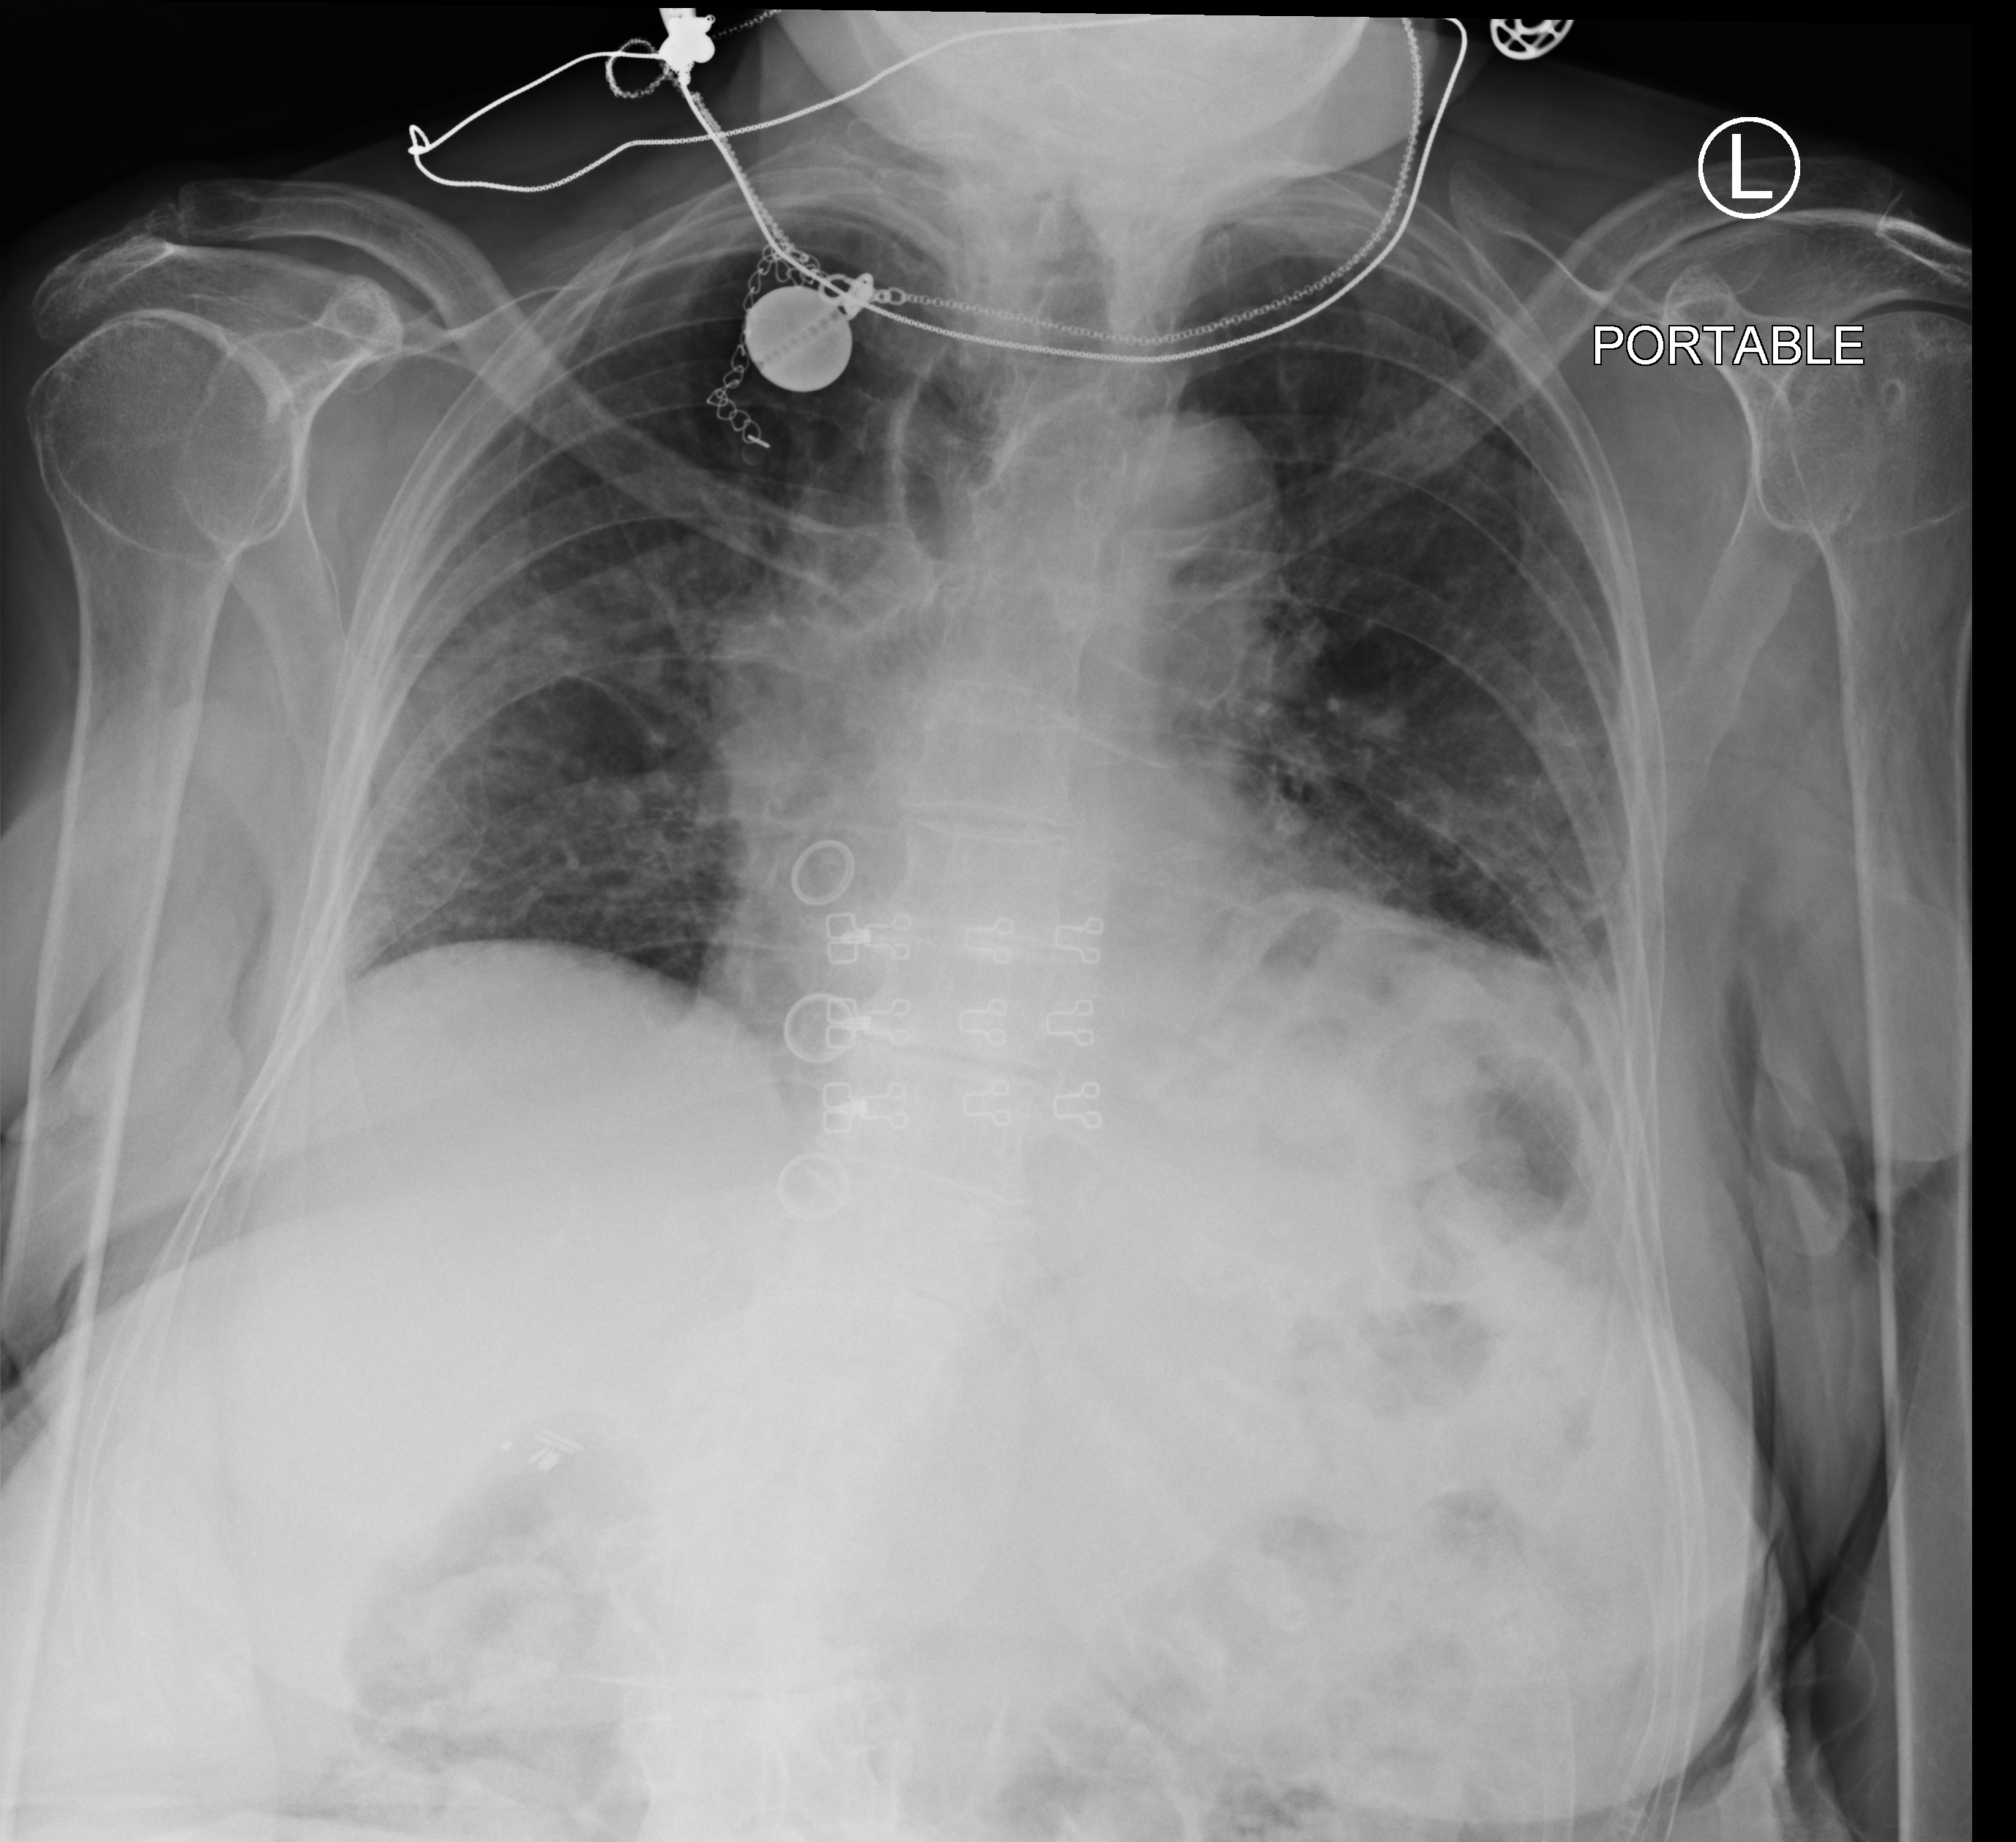
Bedside chest radiograph (computed radiography), anteroposterior (AP) projection. Patient hospitalised with COVID-19; female, aged 75–90 years.
From the hospital-stay record, not from the radiograph (when in the stay this image was taken is not recorded): admitted to intensive care during this hospital stay: no.